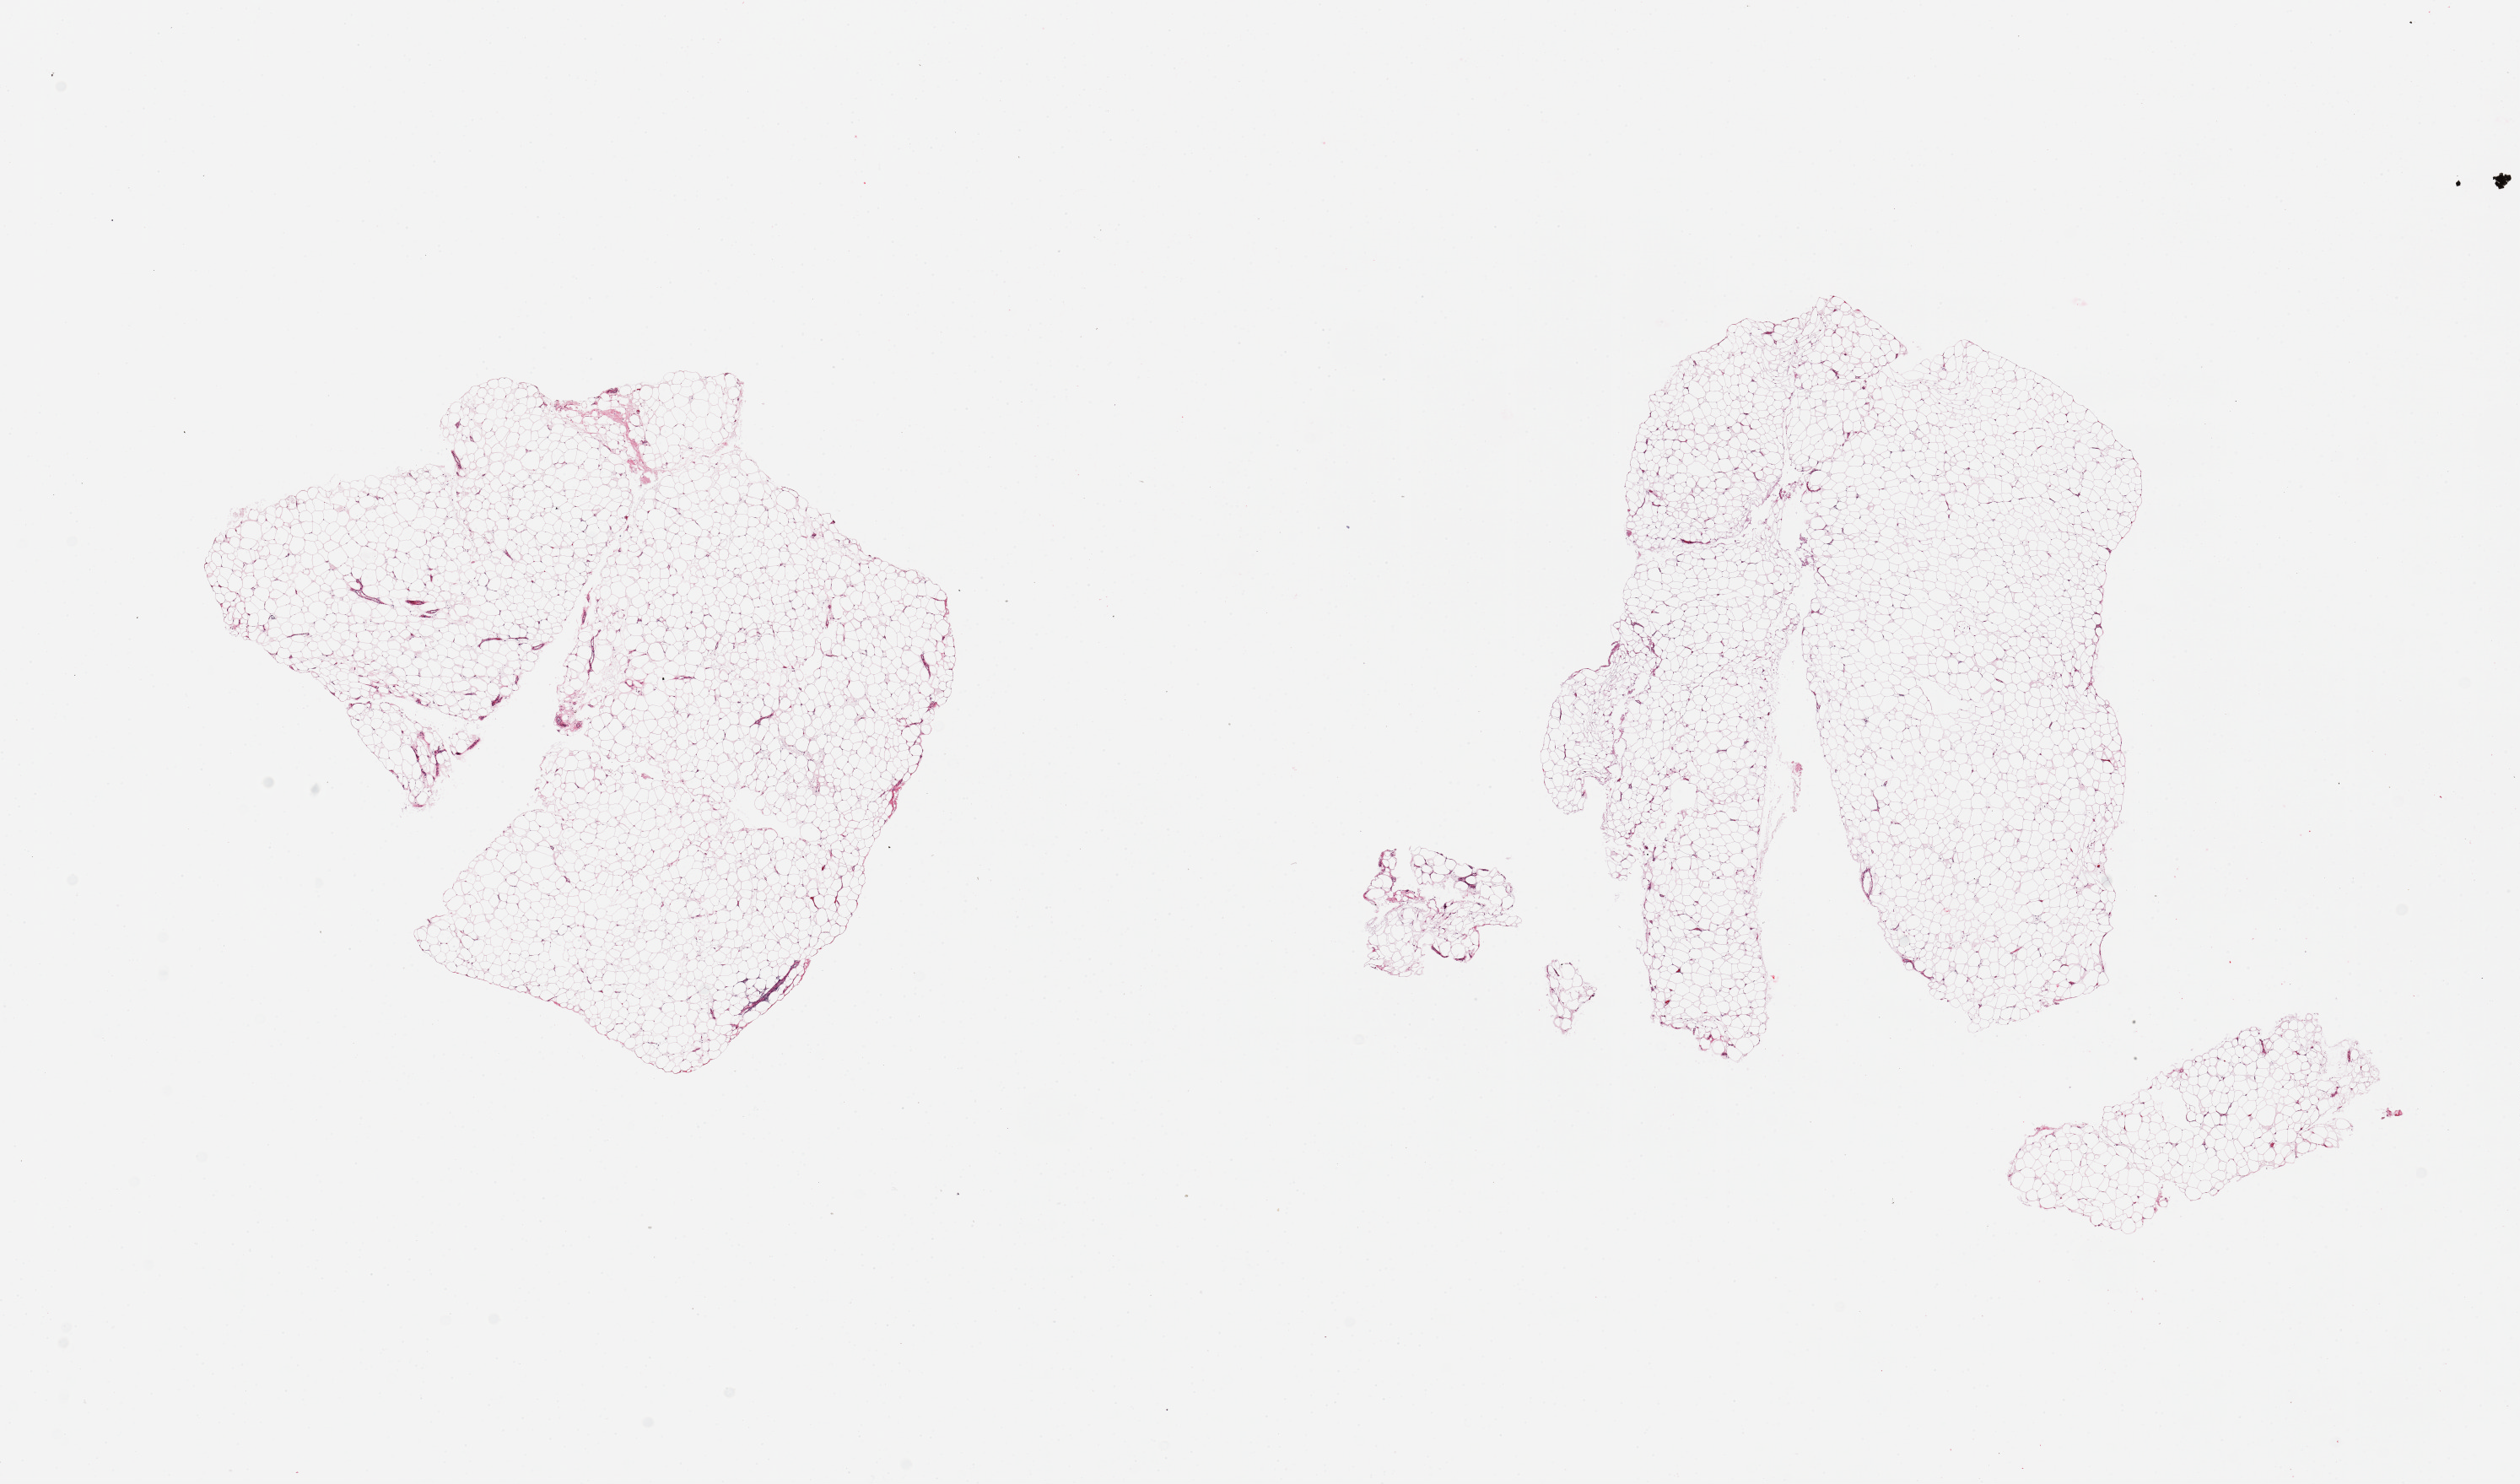
H&E whole-slide image — low-resolution overview of the scanned area, about 23.6 x 13.9 mm. PAXgene-fixed paraffin-embedded (PFPE) section. Sampled site (target tissue): adipose tissue. Tissue donor sample. Donor sex: male.
Review note (as recorded): 2 pieces.